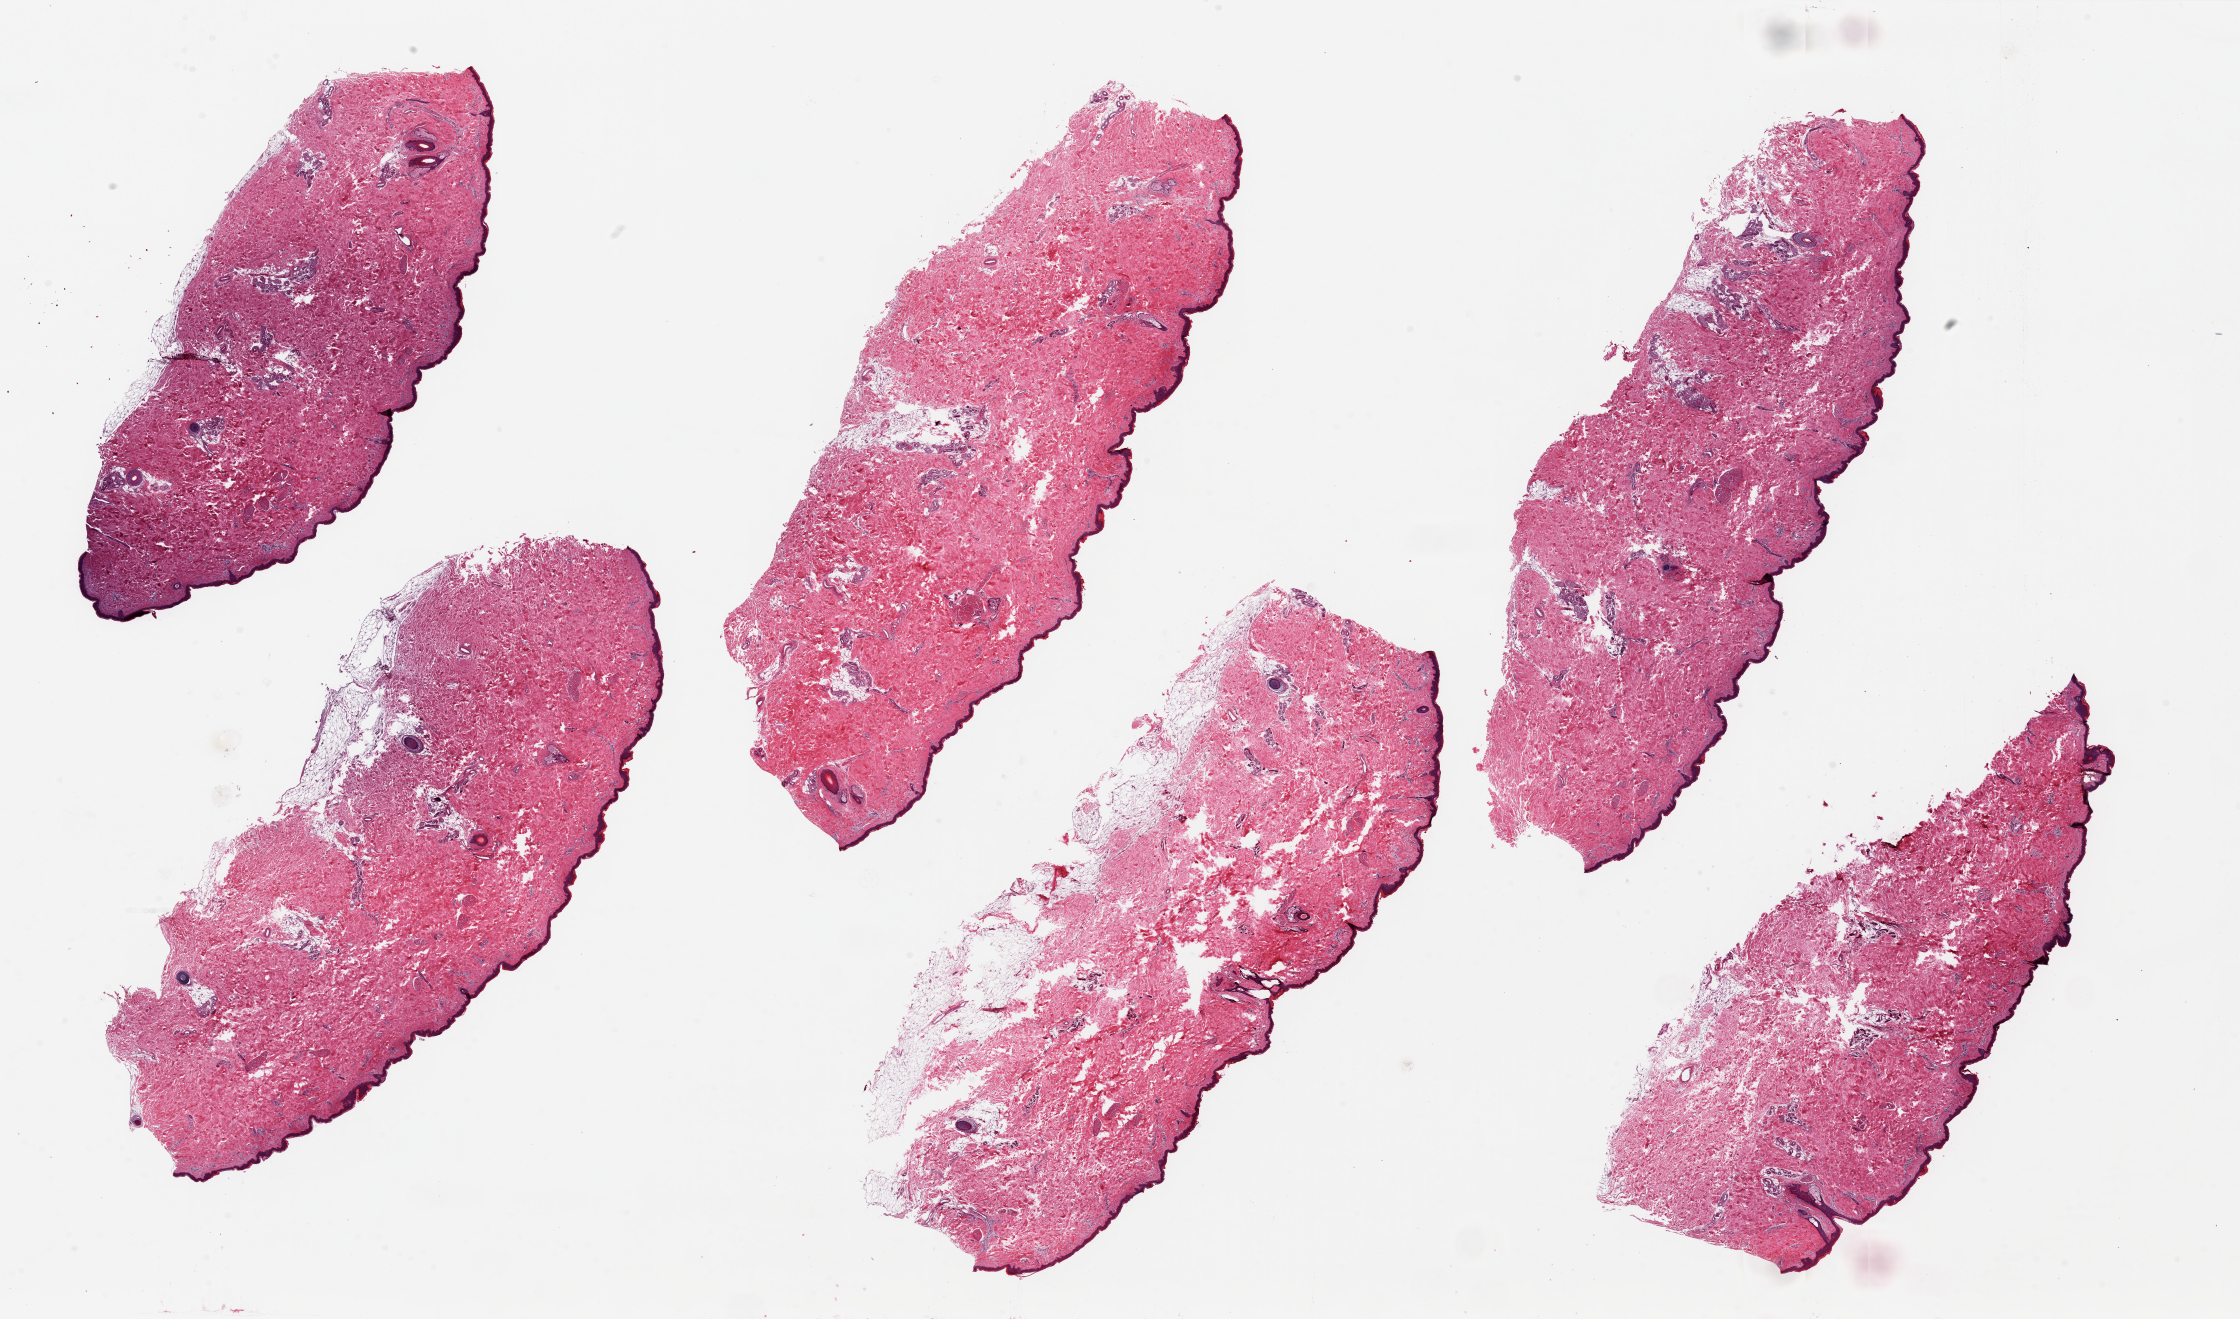
Whole-slide image, hematoxylin and eosin (H&E) stain, brightfield, whole scanned area (about 35.4 x 20.9 mm) shown as a low-resolution overview; PAXgene-fixed, paraffin-embedded tissue; section of skin of lower leg (target tissue); donor tissue sample.
• reviewer comment on this tissue sample: 6 pieces ~11x4mm. Squmous epithelium is ~2-3% of thickness